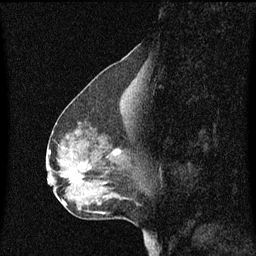
Breast MRI (dynamic contrast-enhanced), one sagittal slice. Position 27 of 60 along the scan axis. Dynamic contrast-enhanced series, image 2 of 3 at this slice position (ordered by acquisition). 1.5 T. TE 4.2 ms, TR 8.4 ms. 256 × 256 image matrix, field of view 200 × 200 mm. Patient: female, 50 years. Case-level facts recorded for this patient, not image findings: setting: breast cancer imaged before/during neoadjuvant chemotherapy; receptor status: HR-positive, HER2-negative.
Annotated regions visible in this slice (semi-automatically segmented with operator editing):
- analysis volume of interest (the breast-tissue region the enhancement analysis was run in; not a lesion): bounding box <61,144,129,189> (left, top, right, bottom; pixels)
- tumour enhancement mask (voxels above the 70 % enhancement threshold inside the analysis volume of interest): <71,150,121,183>